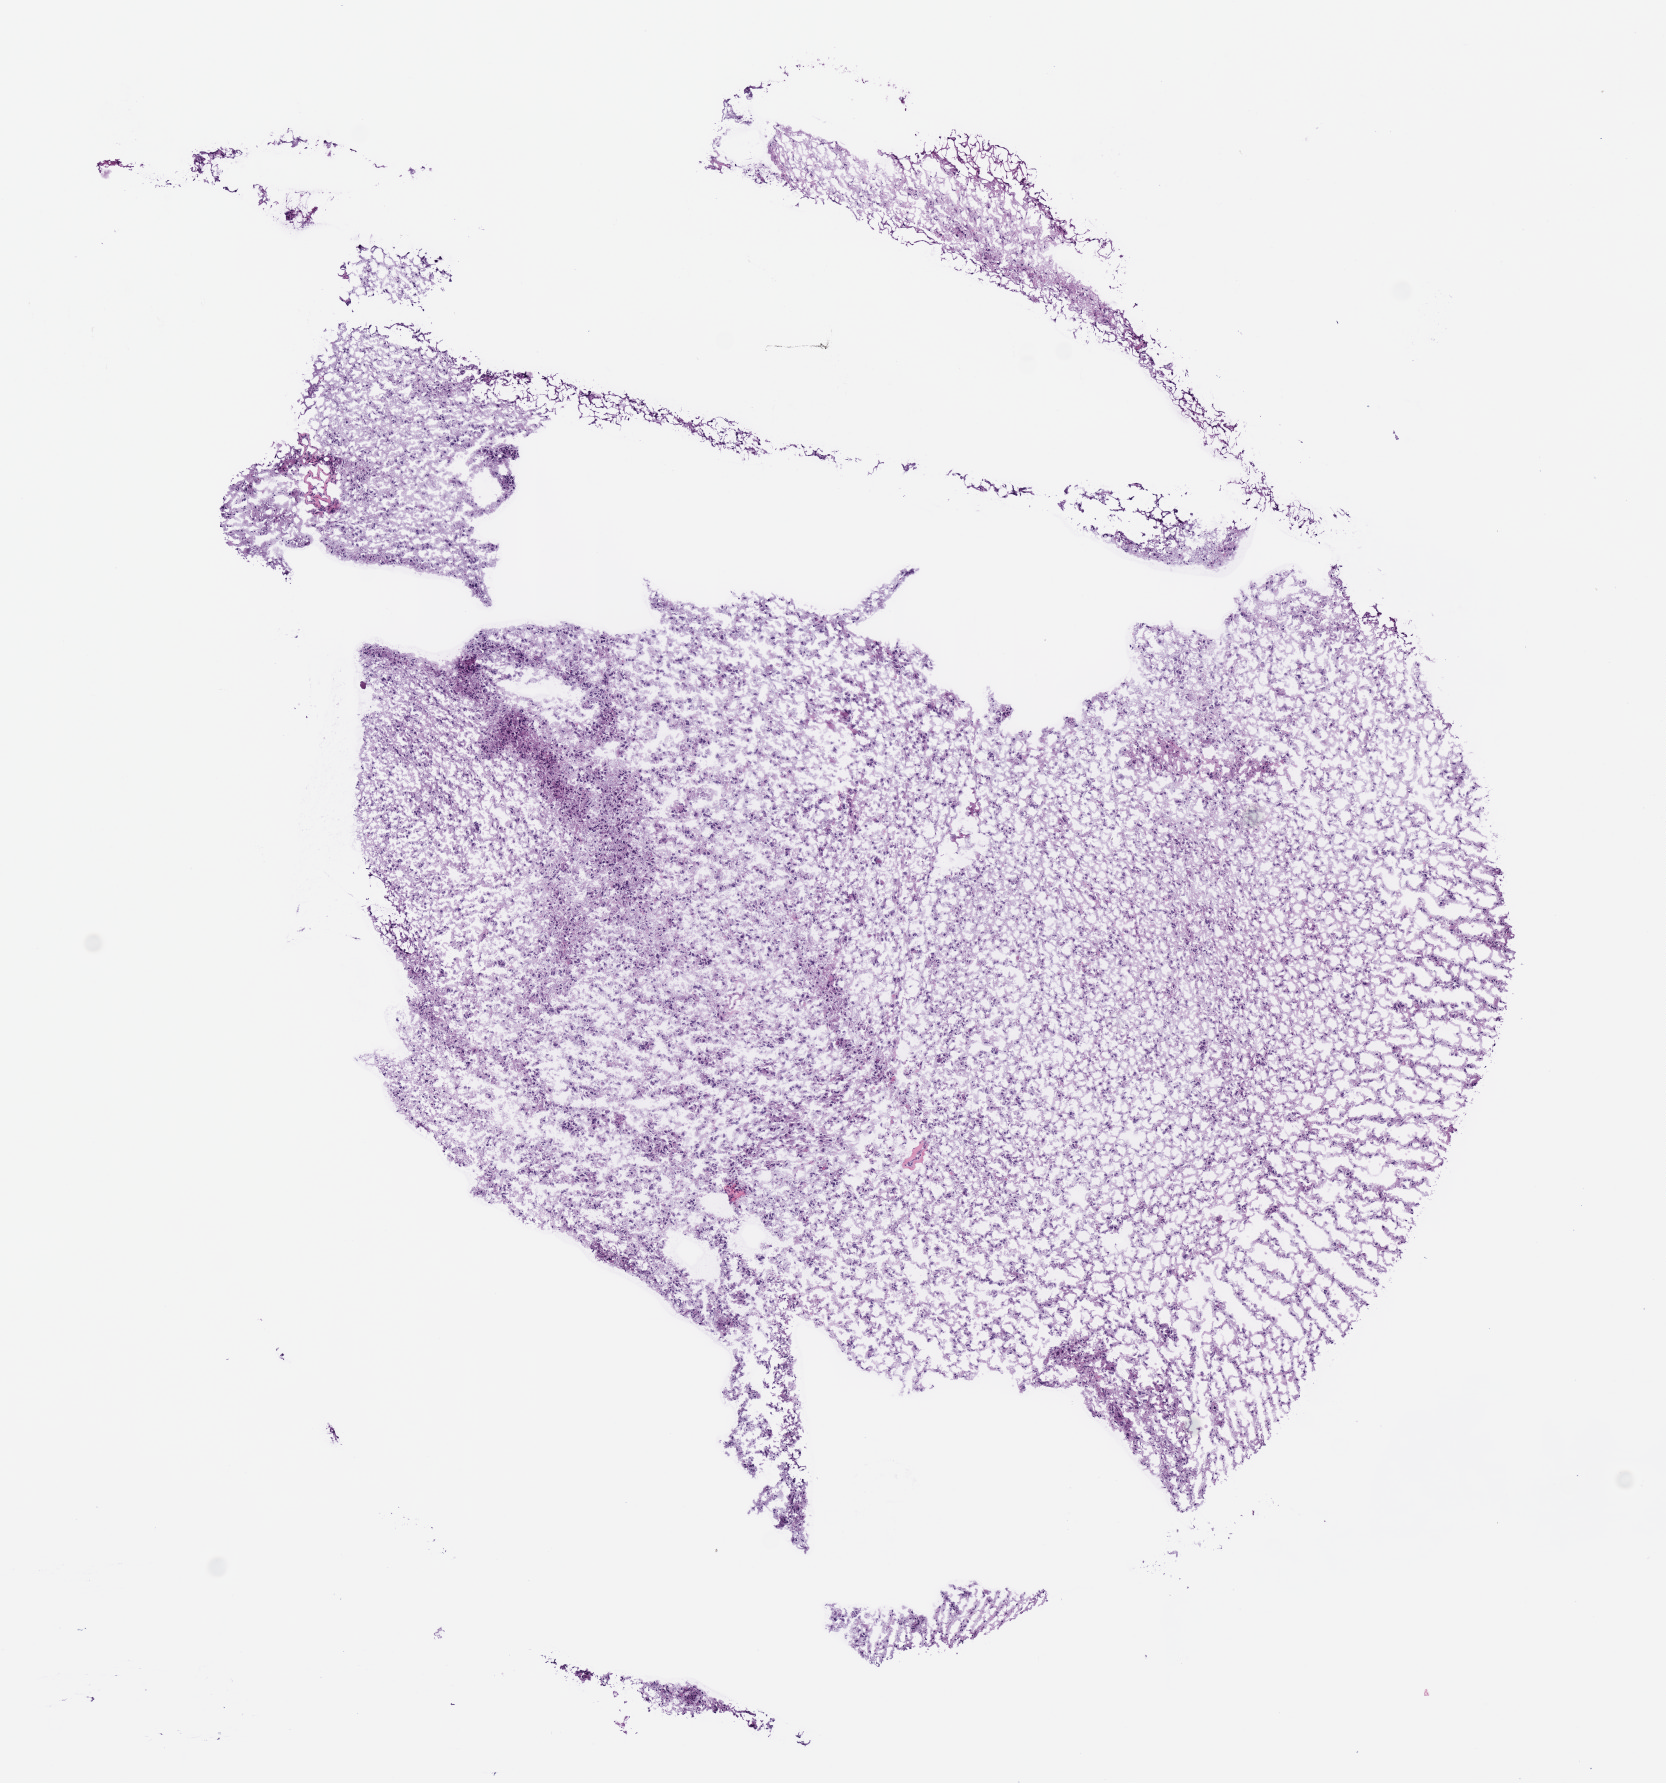
Digitized H&E tissue section (whole slide) — a low-resolution overview of the entire scanned area, about 6.6 x 7.0 mm. Frozen section from the bottom of the tissue portion. Primary tumour sample from the brain. Male, age 34 years at initial diagnosis. Histologic grade: G3 (poorly differentiated). Pathologist review of this section (percent, as recorded): tumour cells 100%, tumour nuclei 80%, normal cells 0%, stromal cells 0%, necrosis 0%.
* histologic diagnosis: Mixed glioma (cerebrum)
* laterality: right